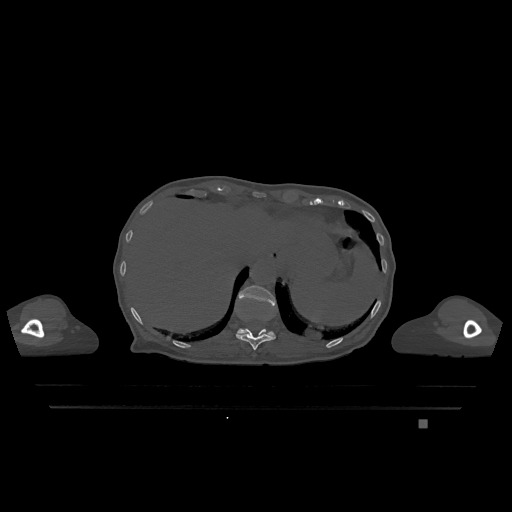
CT including the spine, one axial slice; slice 571 of 1317 in the series (ordered by position); bone window (W 1800 / L 400 HU); 0.5 mm slice thickness; 512 × 512 image matrix, field of view 500 × 500 mm. Patient: female, 74 years. From the clinical record (not read from this slice): primary cancer: lung.
Outlined on this slice (semi-automatic segmentation, software-assisted and operator-edited):
- T11 vertebra: bounding box (x1, y1, x2, y2) in pixels: (236, 329, 276, 350)
- T12 vertebra: (237, 285, 276, 337)